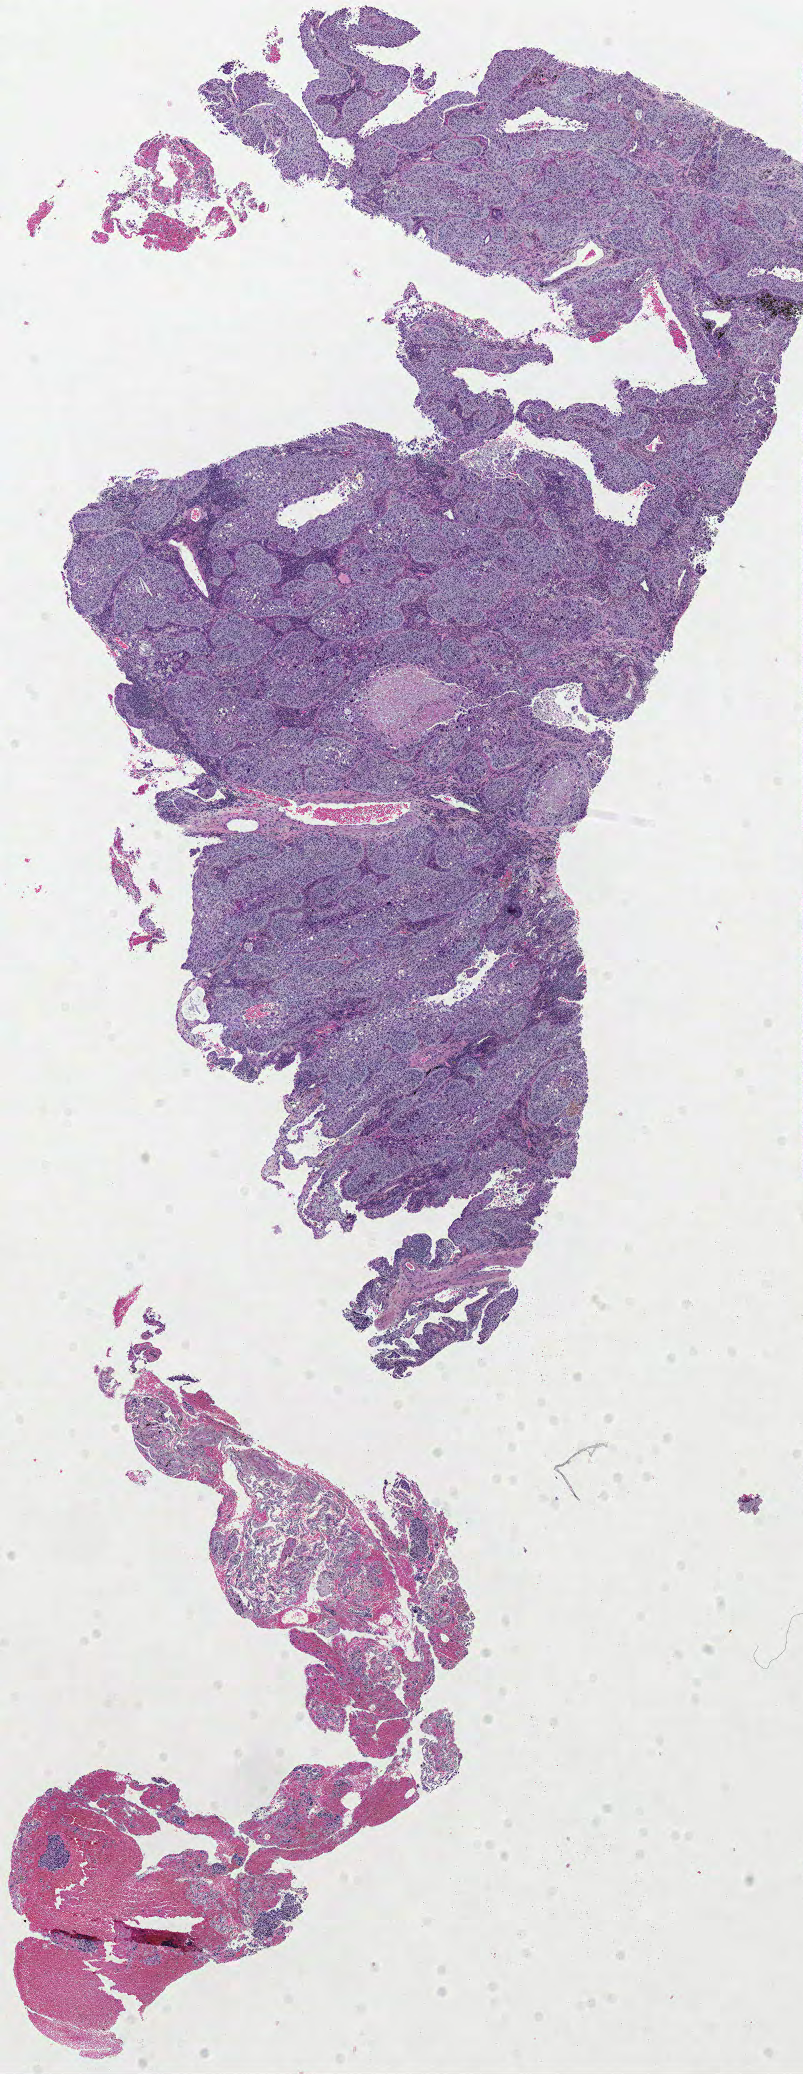
Hematoxylin and eosin (H&E) stained whole-slide image, whole scanned area (about 6.3 x 16.3 mm, acquisition: 40x scan) shown as a low-resolution overview, formalin-fixed paraffin-embedded (FFPE) diagnostic section, primary tumour sample from the lung. Male patient; age at initial diagnosis 66 years.
AJCC pathologic stage: IB (6th edition). Diagnosis: Squamous cell carcinoma, NOS.